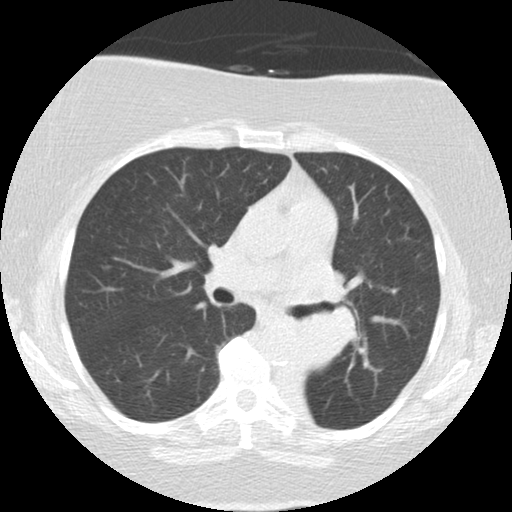
Low-dose screening chest CT, one axial slice; position 79 of 136 along the scan axis; 120 kVp; lung window (W 1500 / L -600 HU); 2.5 mm slice thickness; 512 × 512 image matrix, field of view 309 × 309 mm.
Structures marked on this image (expert manual segmentation):
- lesion 2 (tumor, mediastinum): bounding box (x1, y1, x2, y2) in pixels: (299, 270, 357, 369)